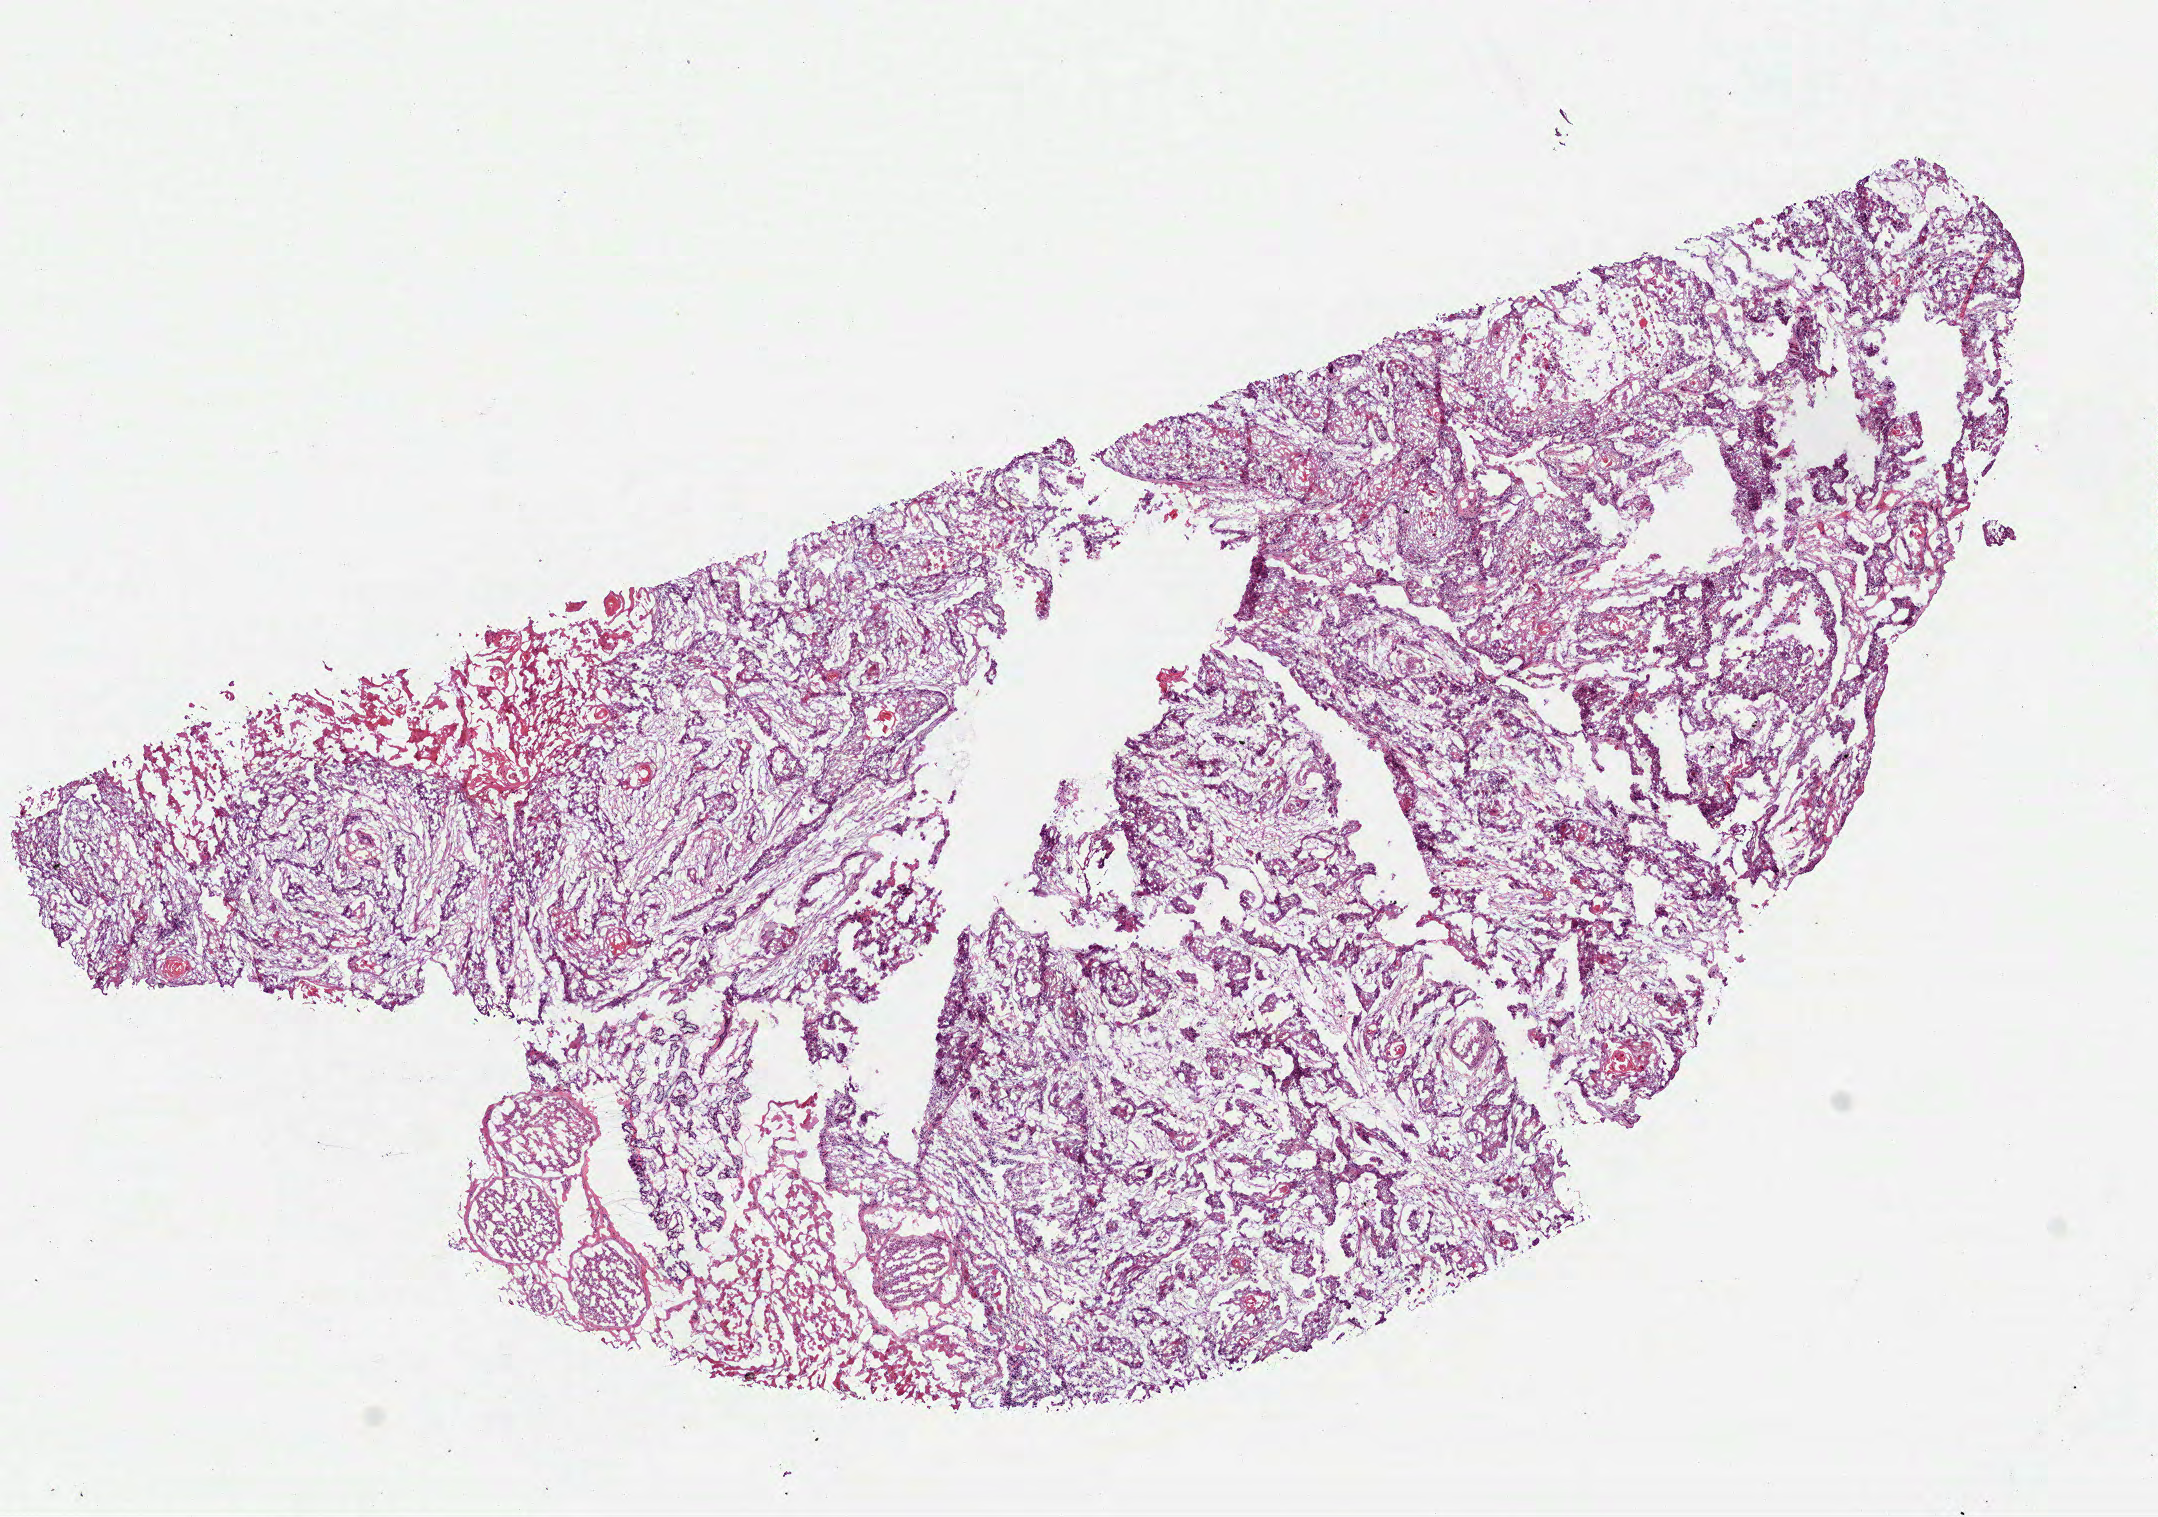
Digitized H&E-stained tissue section (whole slide), a low-resolution overview of the entire scanned area, about 8.7 x 6.1 mm. Frozen section from the top of the tissue portion. Sample: primary tumour, head and neck. Male, age 57 years at initial diagnosis. Histologic grade: G2 (moderately differentiated). Composition of this section per pathologist review: tumour cells 84%, tumour nuclei 80%, normal cells 11%, necrosis 5%. Infiltration values recorded for this section: lymphocyte infiltration 7%, neutrophil infiltration 7%.
AJCC pathologic stage: IVA (7th edition). Histologic diagnosis: Squamous cell carcinoma, NOS (tongue, NOS).